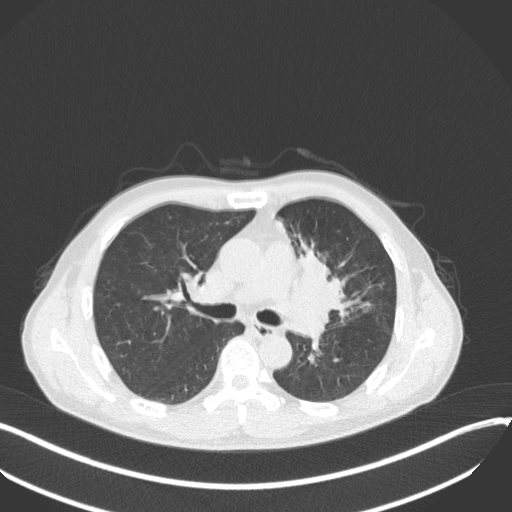
Chest CT, one axial slice. Slice 205 of 411 in the series (ordered by position). Reconstruction kernel B31f. 120 kVp. Lung window (W 1500 / L -600 HU). 512 × 512 image matrix, field of view 400 × 400 mm. Patient: male, 56 years. Case-level facts recorded for this patient, not image findings: clinical TNM (as recorded): T2a N0 M0.
Outlined on this slice (bounding box drawn by a radiologist):
- lung tumour (recorded histology: squamous cell carcinoma): bounding box <292,249,353,328> (left, top, right, bottom; pixels)